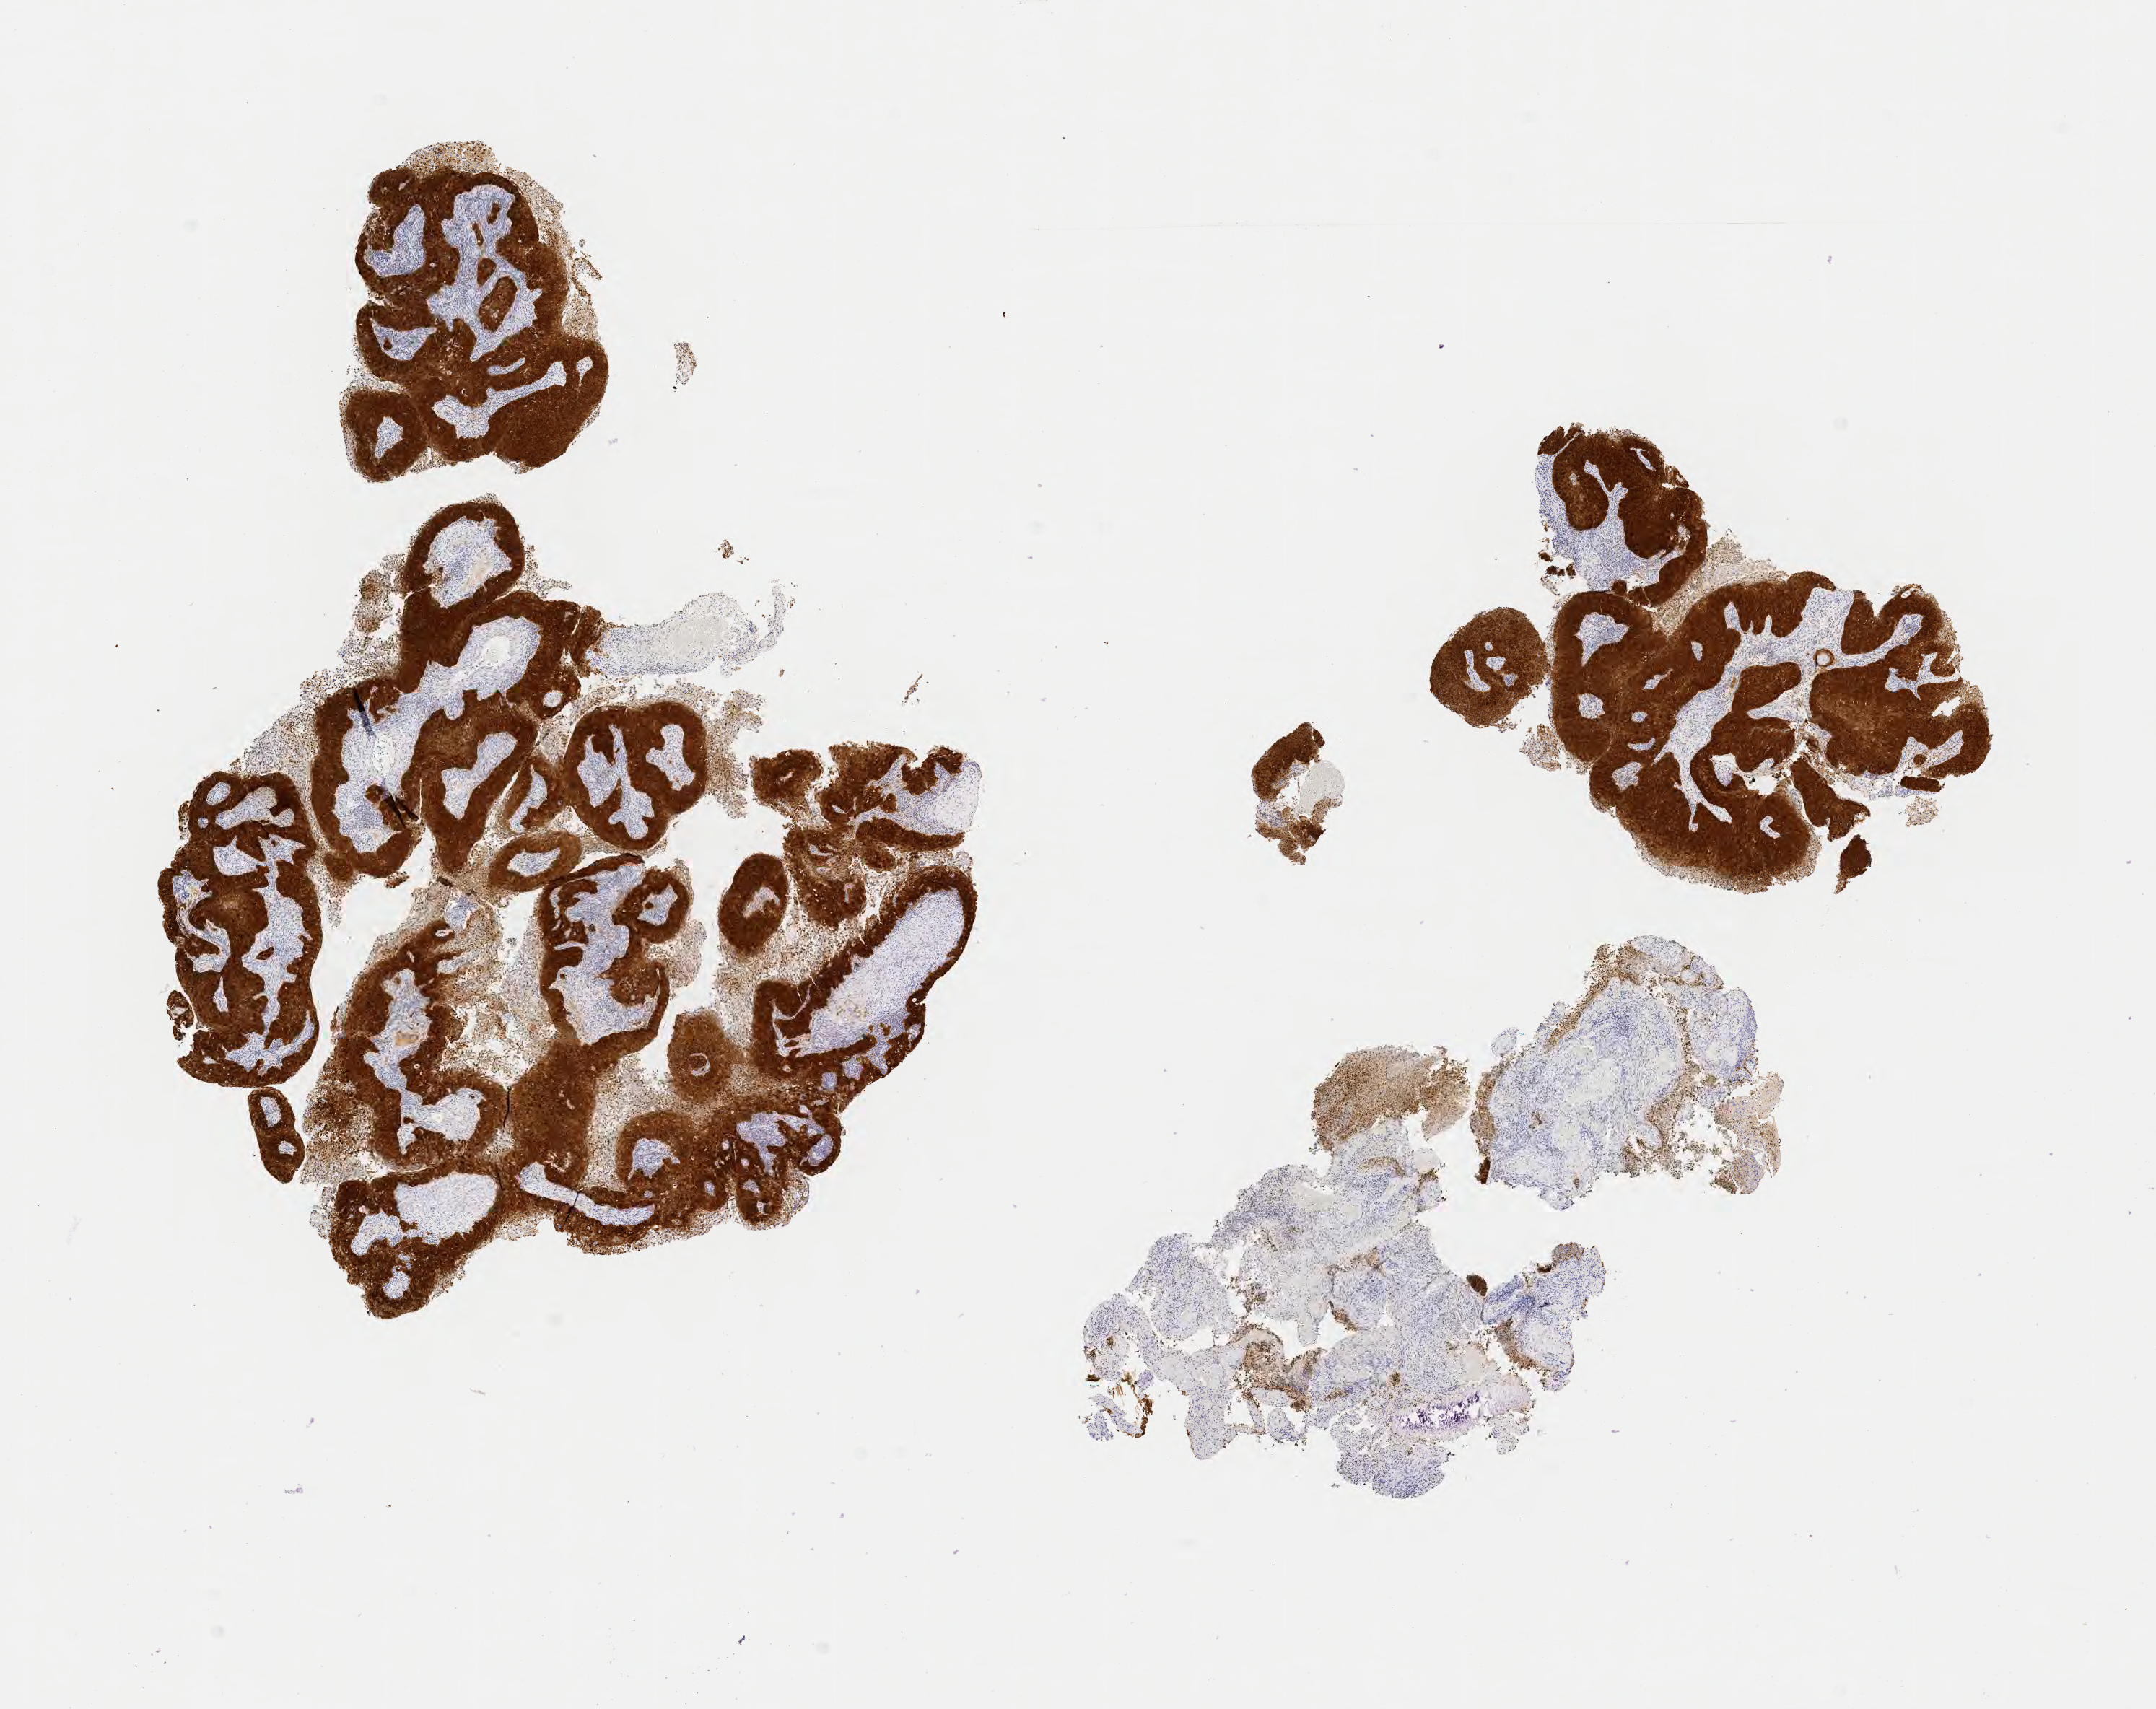
IHC for p16 (p16INK4a), whole-slide image, low-resolution overview of the scanned area, about 12.1 x 9.6 mm. Specimen: tumor tissue. Site: cervix. Female patient, aged 59.
Diagnosis: Squamous cell carcinoma, large cell, nonkeratinizing, NOS.